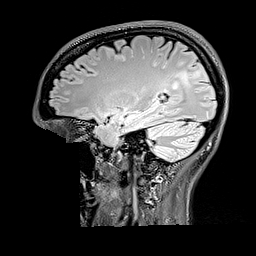
Brain MRI from a brain-tumour surgery series, one sagittal slice. Position 113 of 176 along the scan axis. T2 FLAIR. 256 × 256 image matrix, field of view 256 × 256 mm. Case-level facts recorded for this patient, not image findings: histopathology: Oligodendroglioma; WHO grade: 2; IDH mutation: yes; tumour location: Right Parietal.
Structures marked on this image (expert manual segmentation):
- tumour: bounding box [x1, y1, x2, y2] px = [171, 82, 178, 91]